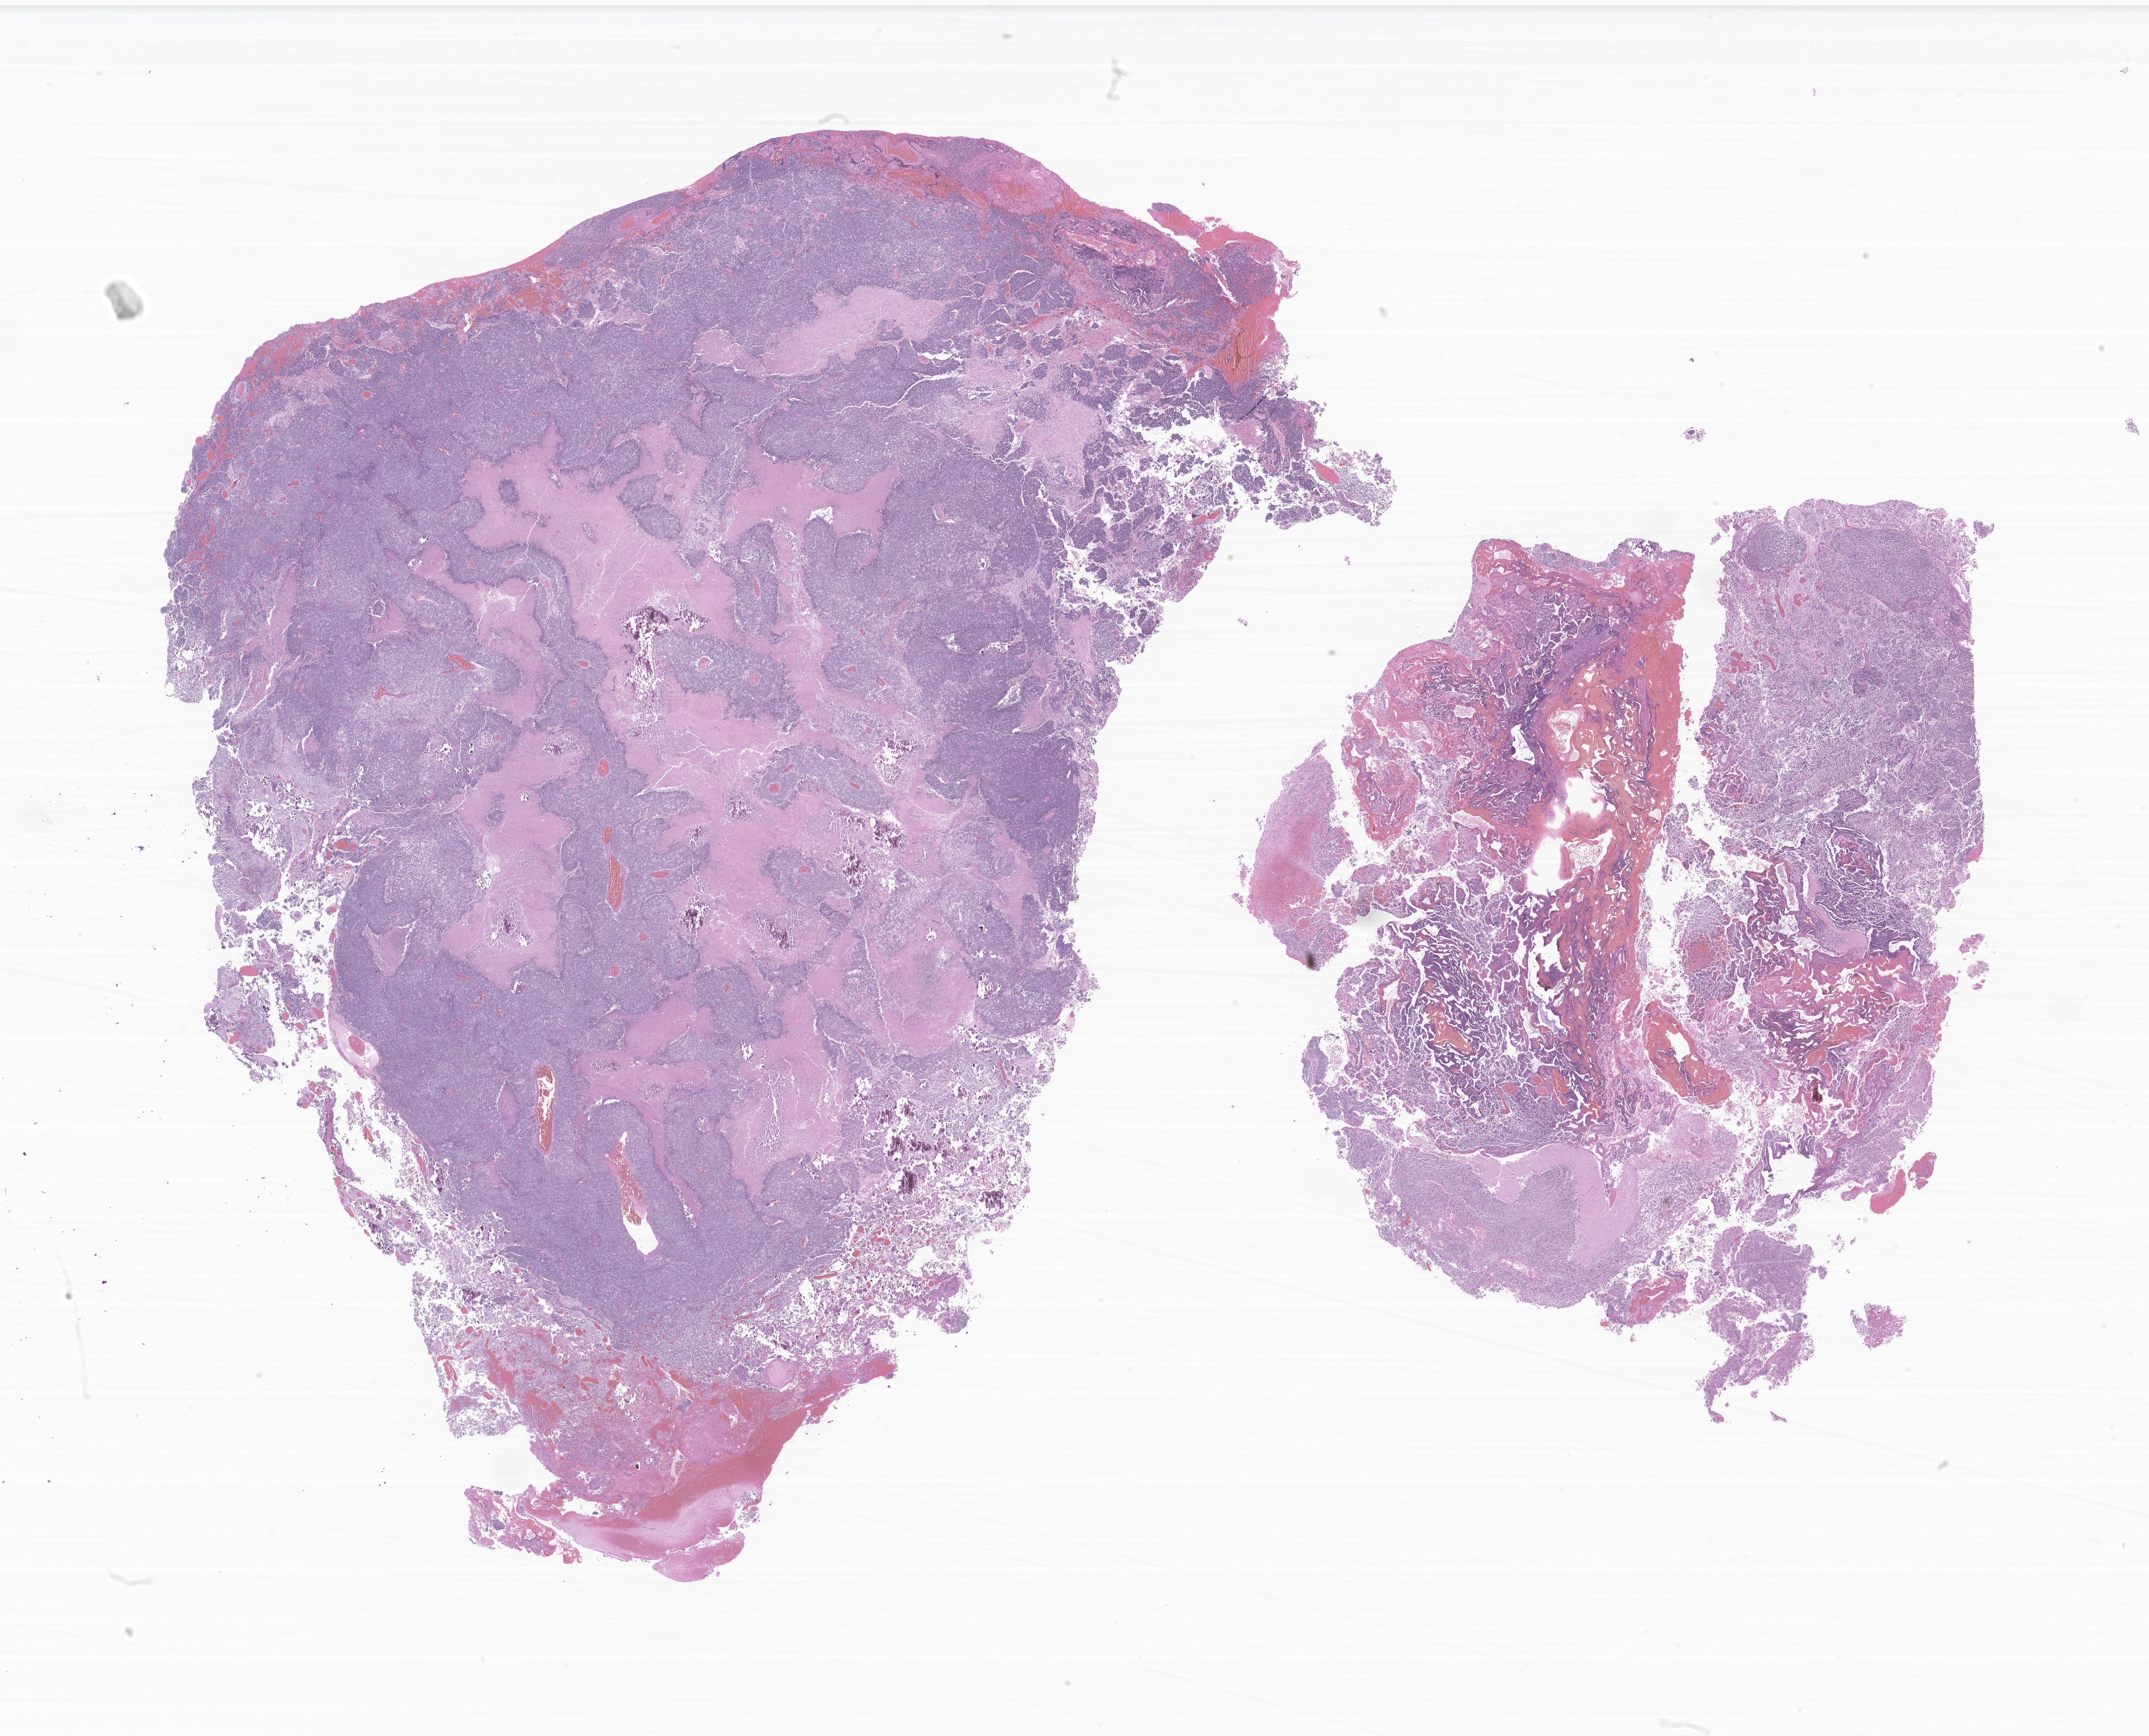
Haematoxylin and eosin whole-slide image of tumor tissue from the cerebellum, shown as a low-resolution overview of the whole scanned area (about 26.0 x 21.0 mm); FFPE section. Male patient, age 86 months (7 years 2 months).
- diagnosis: Medulloblastoma, NOS